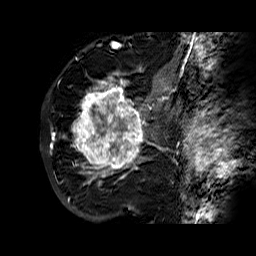
Breast MRI (dynamic contrast-enhanced), one sagittal slice; slice 41 of 60 in the series (ordered by position); dynamic contrast-enhanced series, time point 2 of 6 at this slice position (early post-contrast); 1.5 T; TE 6.3 ms, TR 32.4 ms; 4 mm slice thickness; 256 × 256 image matrix, field of view 200 × 200 mm. Female patient. From the clinical record (not read from this slice): setting: breast cancer imaged before/during neoadjuvant chemotherapy; receptor status: HR-positive, HER2-negative.
Structures marked on this image (semi-automatic segmentation, software-assisted and operator-edited):
- analysis volume of interest (the breast-tissue region the enhancement analysis was run in; not a lesion): bounding box (x1, y1, x2, y2) in pixels: (71, 72, 177, 183)
- tumour enhancement mask (voxels above the 100 % enhancement threshold inside the analysis volume of interest): (71, 73, 167, 183)